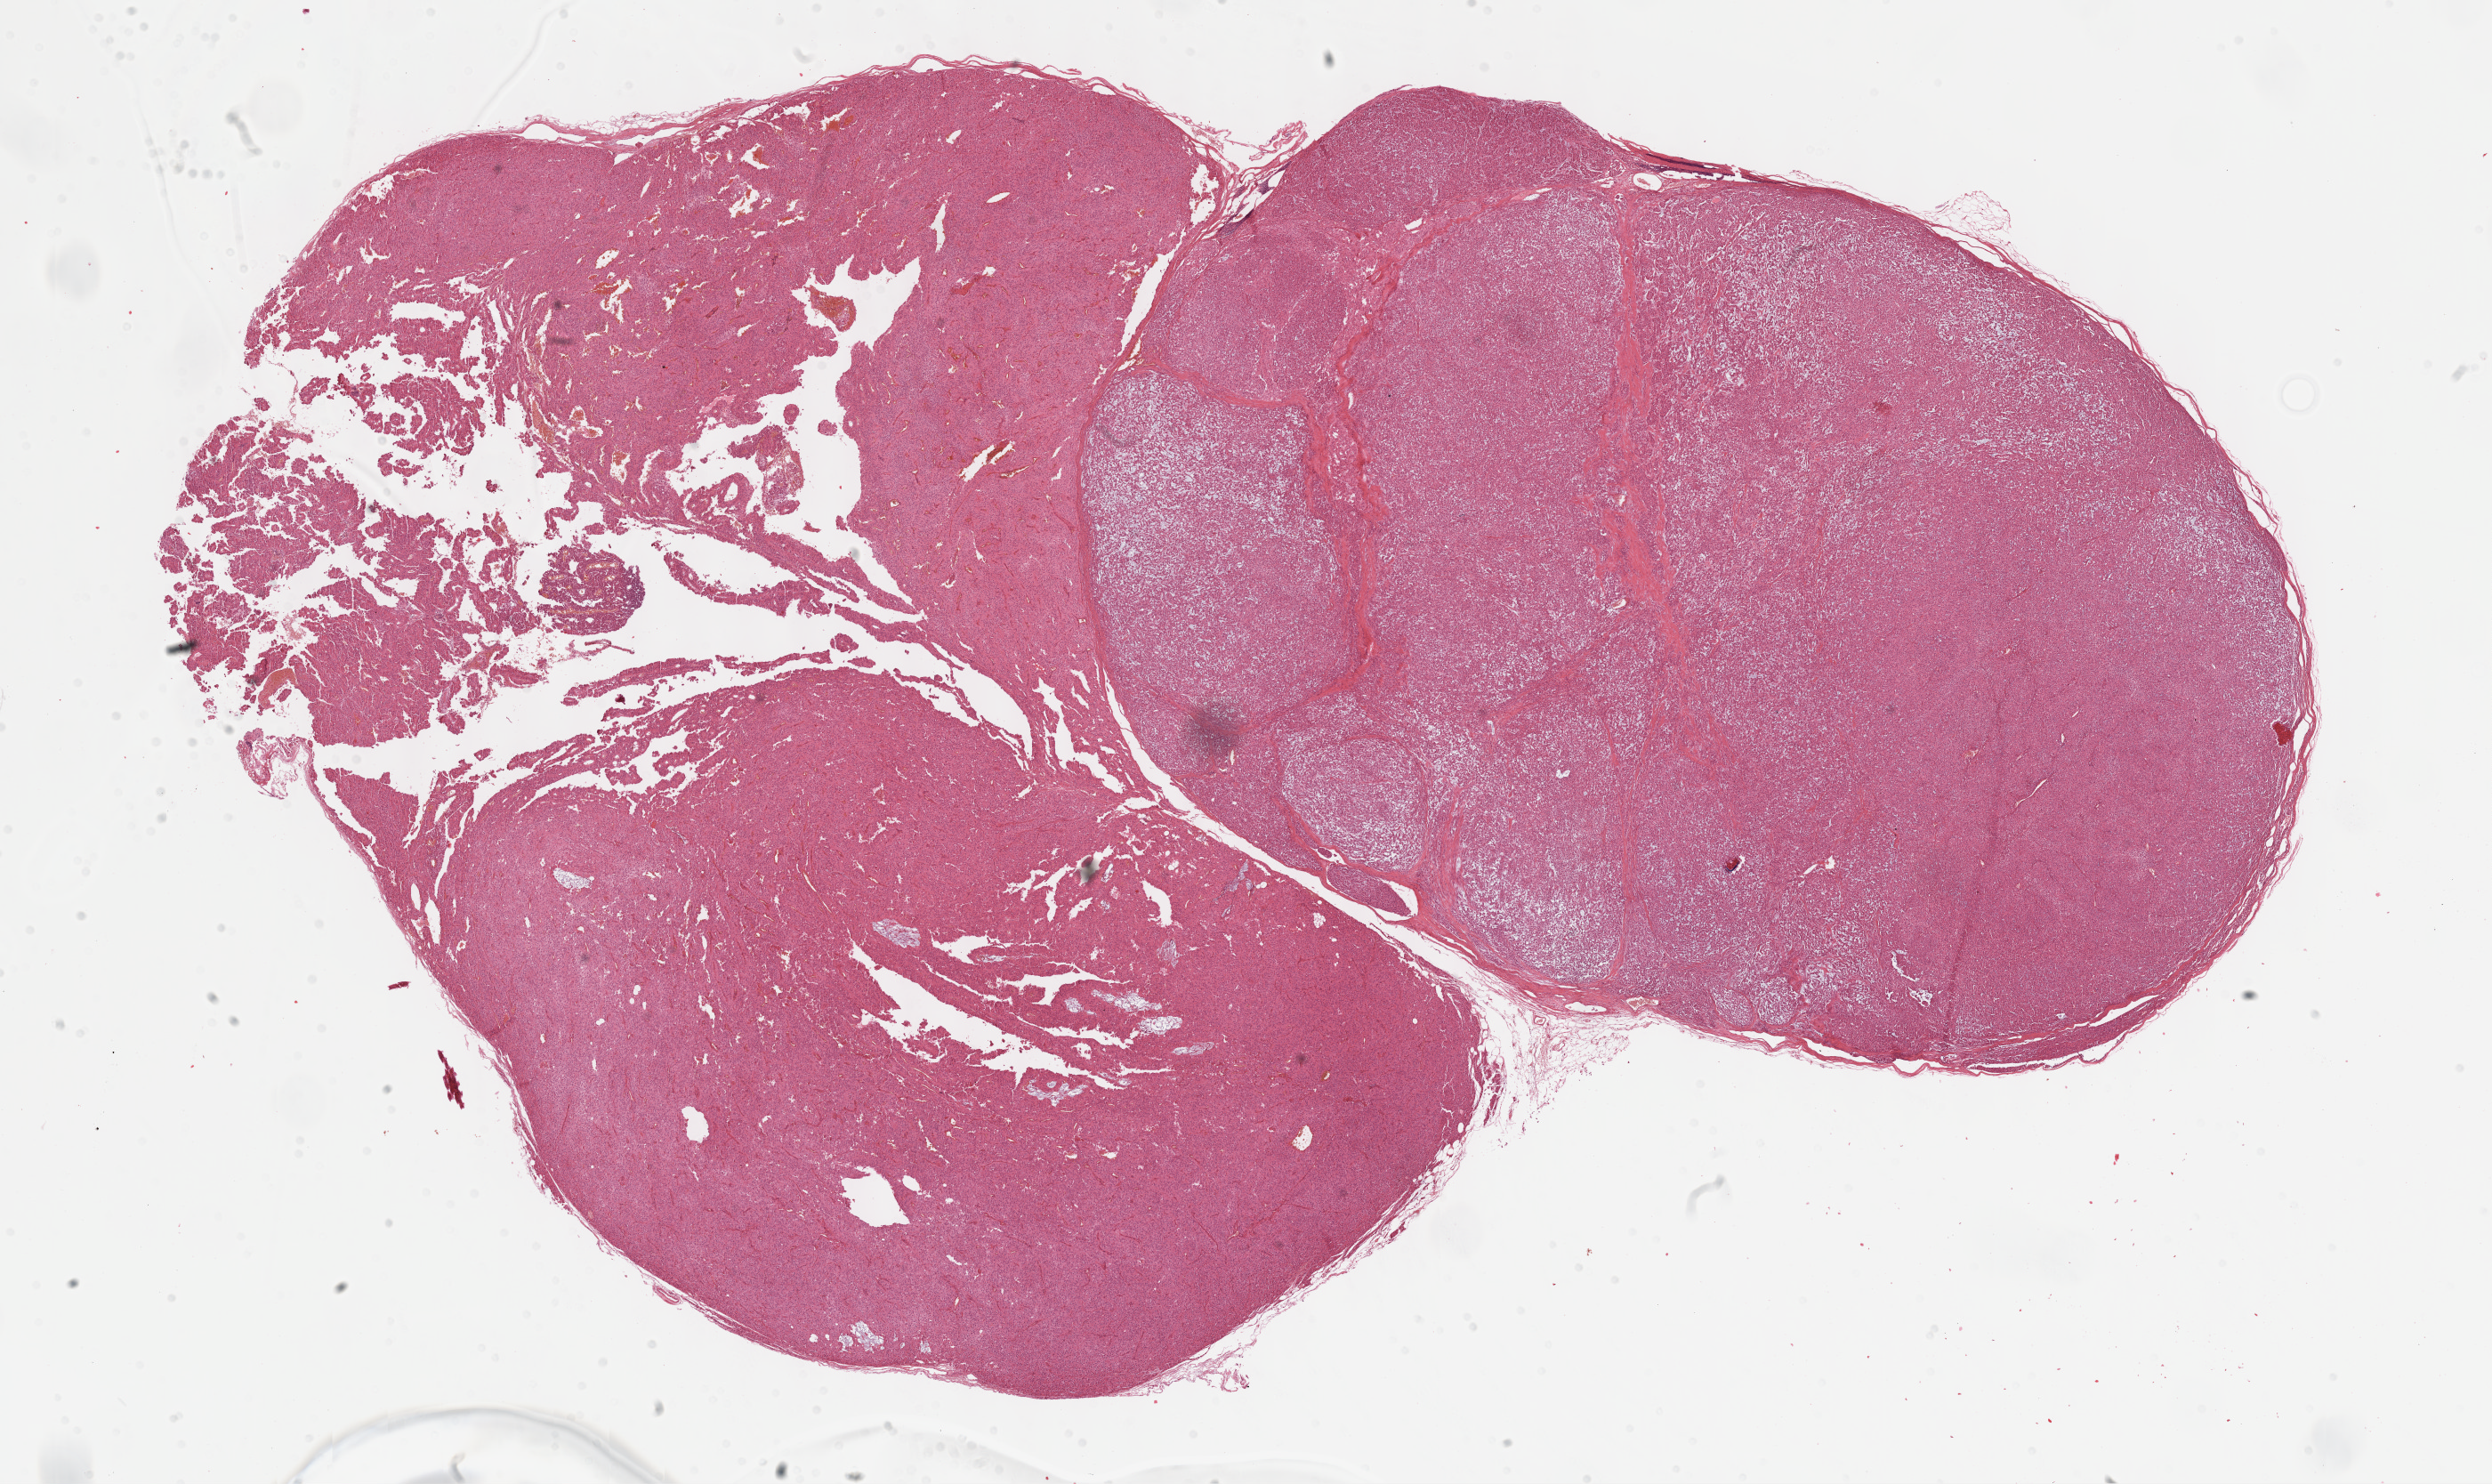
Hematoxylin and eosin (H&E) stained whole-slide image — whole scanned area (about 22.7 x 13.5 mm, from a 40x scan) shown as a low-resolution overview; formalin-fixed paraffin-embedded (FFPE) diagnostic section; sample: primary tumour, adrenal cortex. Patient: male, age at initial diagnosis 61 years.
• diagnosis: Adrenal cortical carcinoma (cortex of adrenal gland)
• lymph nodes positive (case pathology): 6 of 8 examined
• laterality: left